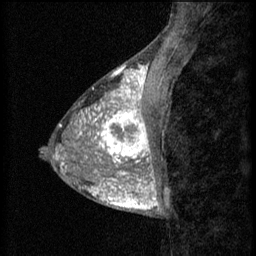
Breast MRI (dynamic contrast-enhanced), one sagittal slice; position 21 of 60 along the scan axis; 3 images stored at this slice position (order not interpretable as contrast timing); 1.5 T; TE 4.2 ms, TR 8.2 ms; 2 mm slice thickness; 256 × 256 image matrix, field of view 180 × 180 mm. Female patient, age 38 years.
Outlined on this slice (semi-automatically segmented with operator editing):
- analysis volume of interest (the breast-tissue region the enhancement analysis was run in; not a lesion): box from (x=95, y=106) to (x=157, y=171) px
- tumour enhancement mask (voxels above the 70 % enhancement threshold inside the analysis volume of interest): (x=95, y=106)–(x=153, y=169)